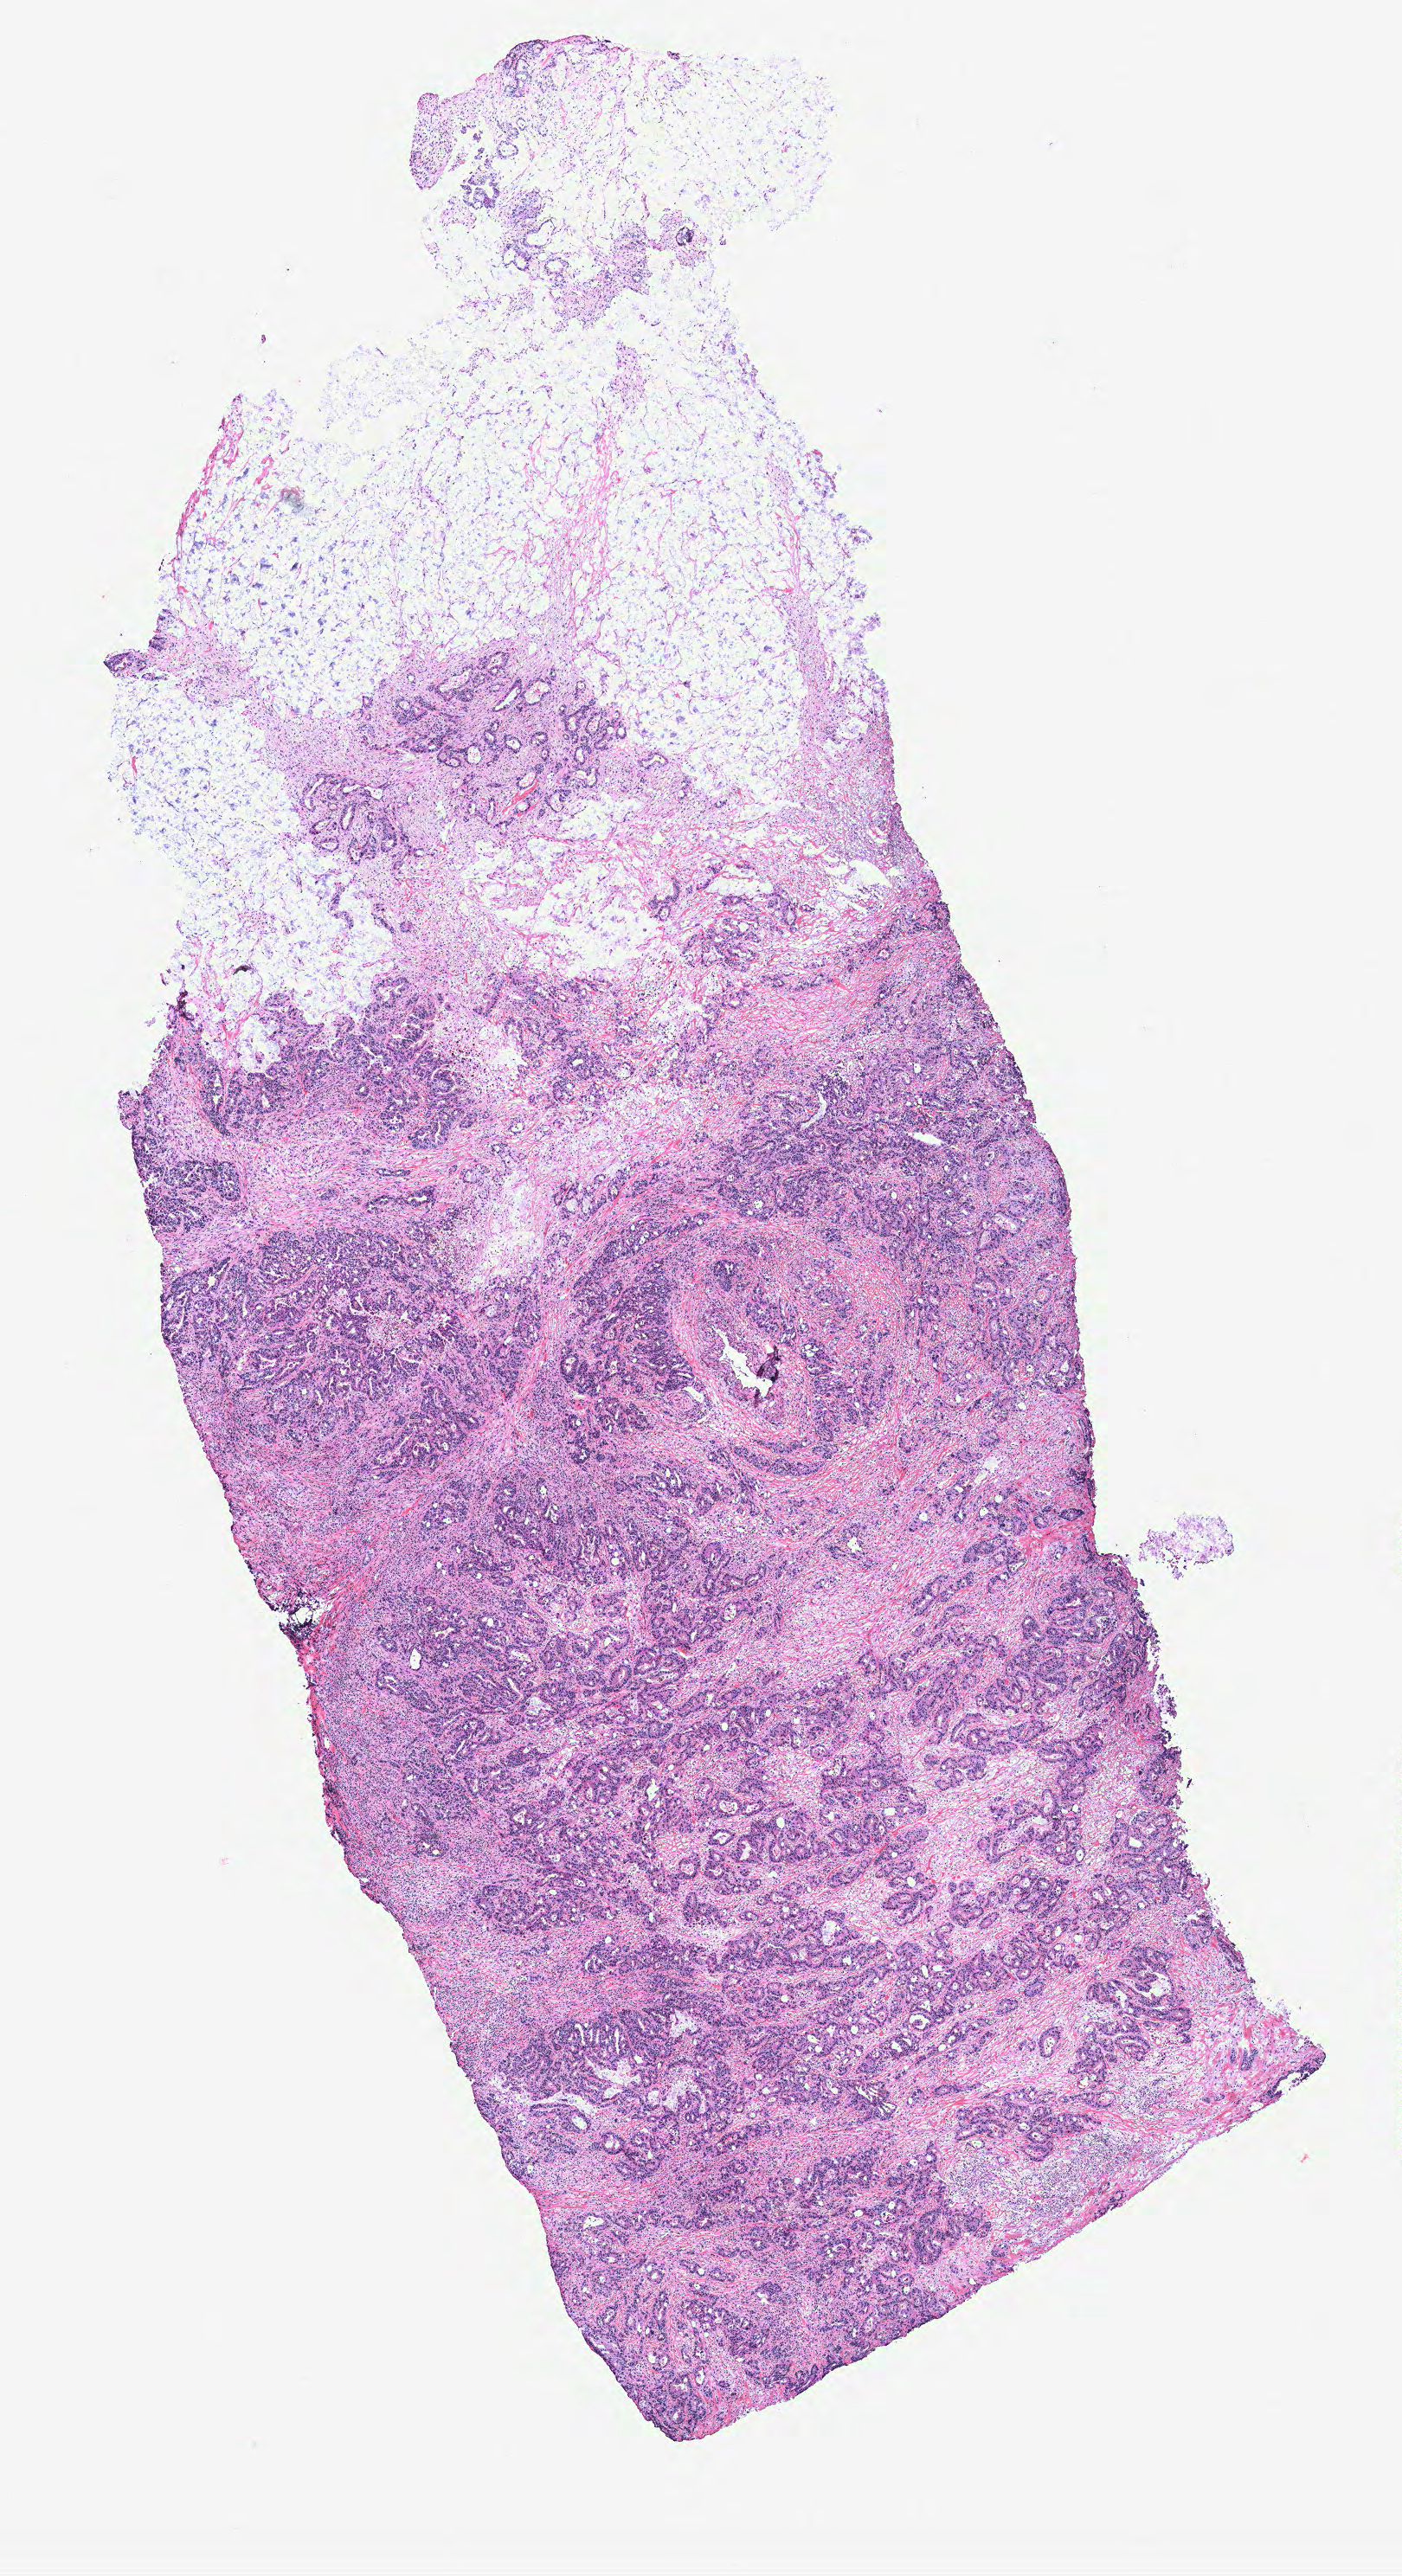
Digitized H&E tissue section (whole slide), a low-resolution overview of the entire scanned area, about 6.5 x 11.9 mm (slide scanned at 40x); colon, tissue type not recorded.
Patient diagnosis (cohort enrolment): colon cancer (colon).